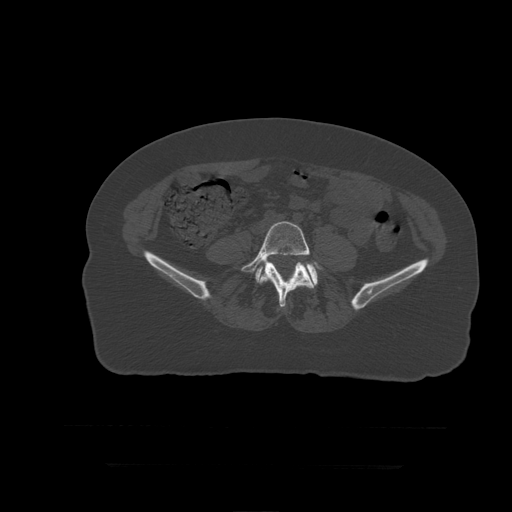
CT including the spine, one axial slice. Slice 72 of 399 in the series (ordered by position). Reconstruction kernel STANDARD. Bone window (W 1800 / L 400 HU). 512 × 512 image matrix, field of view 450 × 450 mm. Patient age 41 years. Case-level facts recorded for this patient, not image findings: primary cancer: breast.
Structures marked on this image (semi-automatically segmented with operator editing):
- L5 vertebra: bounding box (x1, y1, x2, y2) in pixels: (241, 222, 323, 308)